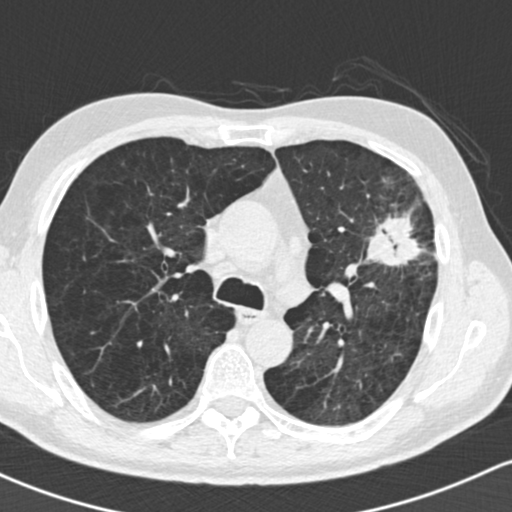
Low-dose screening chest CT, axial slice; first (baseline) screen; lung window (W 1500 / L -600 HU); 2 mm slice thickness; slice 61 of 162 in the series; 512 × 512 image matrix, field of view 318 × 318 mm. Male participant, aged 61 years at enrolment. Former smoker at enrolment.
Expert reader's lesion annotation, box from (x=355, y=186) to (x=453, y=293) px. Reader record for this screening exam (exam-level; its link to the box is not recorded): non-calcified nodule or mass ≥4 mm, left upper lobe, 35 × 35 mm, spiculated (stellate) margins, soft tissue attenuation. Later outcome: lung cancer diagnosed 19 days after this screen — adenocarcinoma, NOS, left upper lobe, well differentiated (G1), stage IIIA (AJCC 6th edition), 45 mm at pathology.